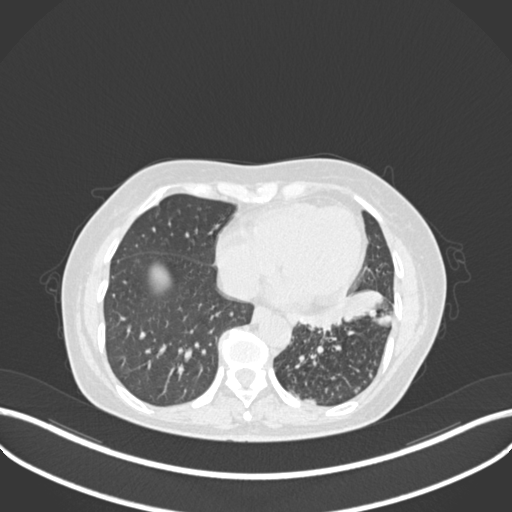
Chest CT, one axial slice. Slice 88 of 270 in the series (ordered by position). Reconstruction kernel B30f. Lung window (W 1500 / L -600 HU). 1 mm slice thickness. 512 × 512 image matrix, field of view 400 × 400 mm. Patient: female, 63 years. From the clinical record (not read from this slice): clinical TNM (as recorded): T1b N0 M0.
Structures marked on this image (bounding box drawn by a radiologist):
- lung tumour (recorded histology: adenocarcinoma): bounding box <302,291,392,332> (left, top, right, bottom; pixels)